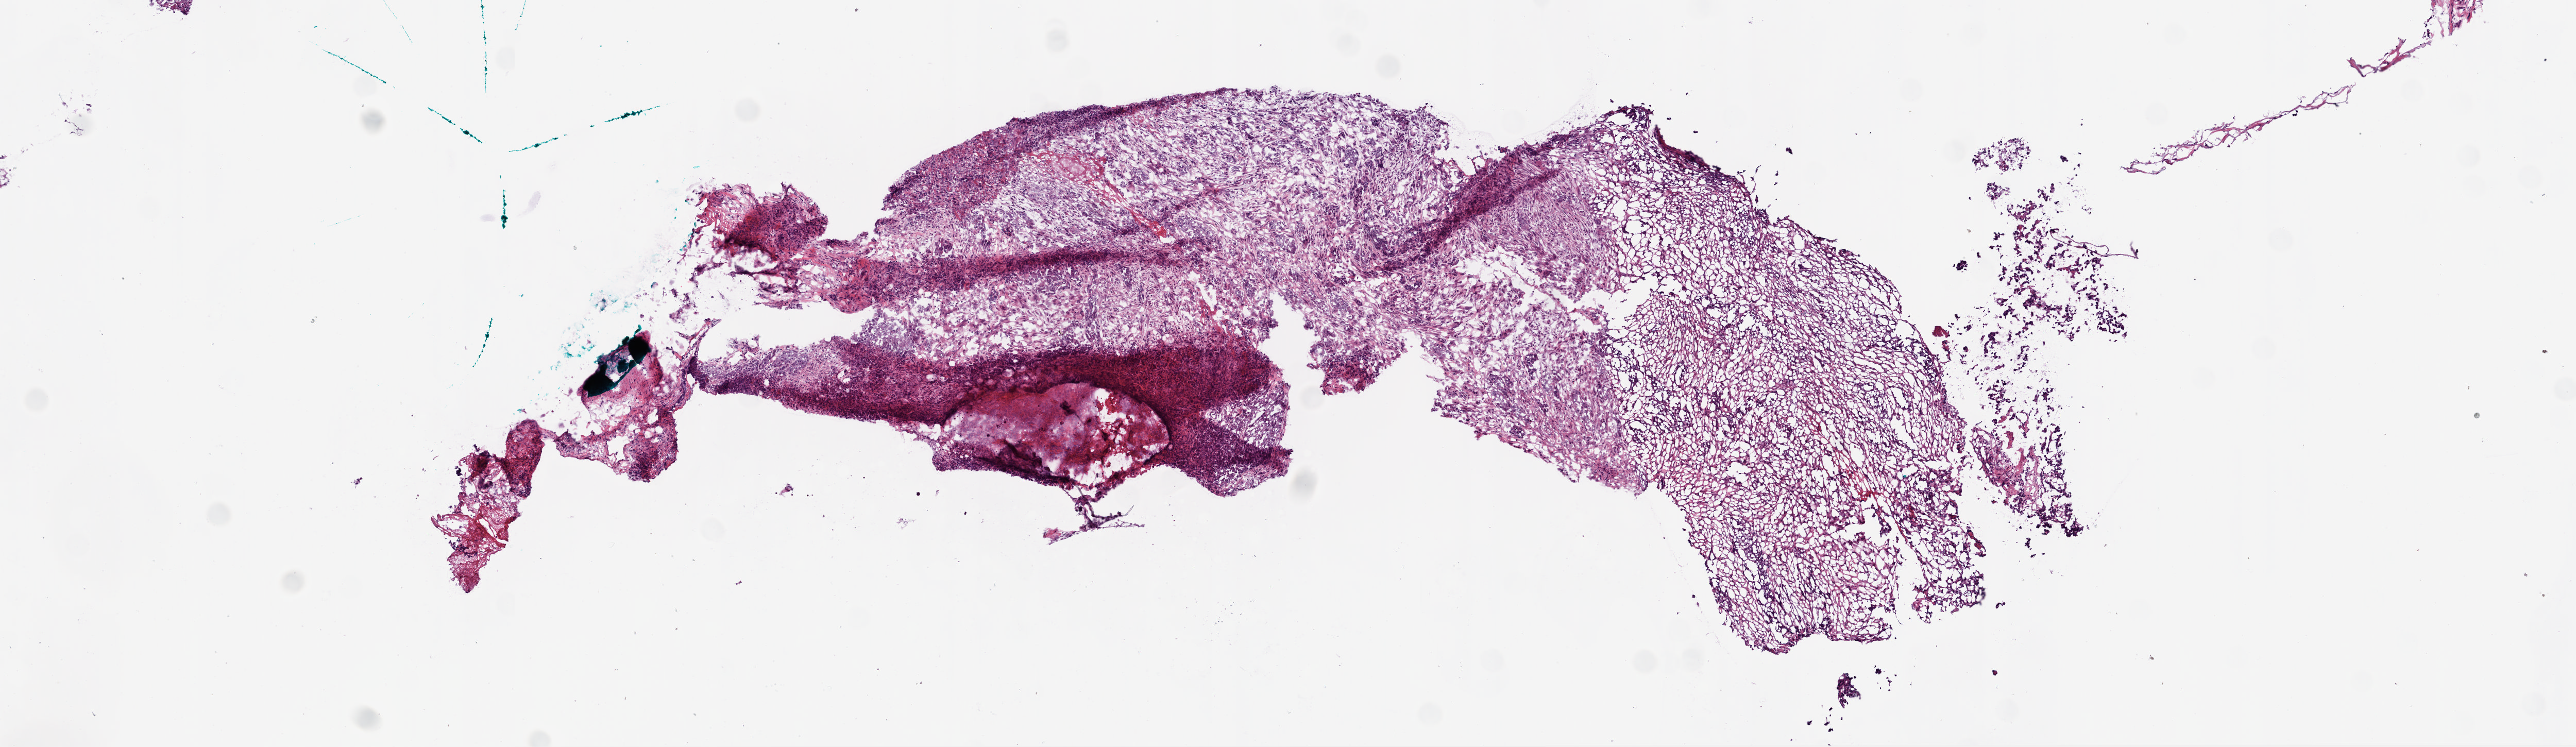
H&E-stained whole-slide image — shown as a low-resolution overview of the whole scanned area (about 10.0 x 2.9 mm, acquisition: 20x scan); frozen section from the bottom of the tissue portion; sample: primary tumour, ovary. Female patient; age at initial diagnosis 45 years. Composition of this section per pathologist review: tumour cells 69%, tumour nuclei 70%.
Pathologic diagnosis: Serous cystadenocarcinoma, NOS.